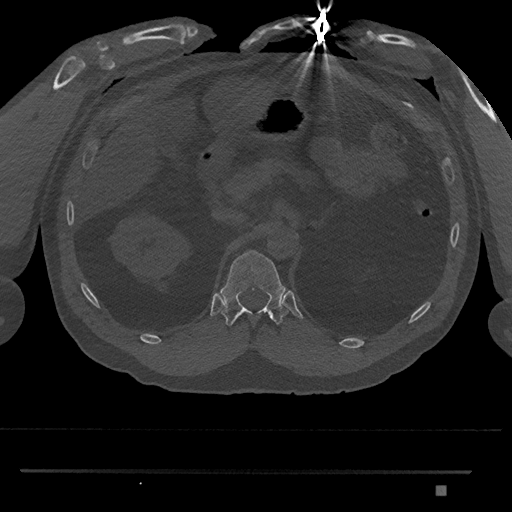
CT including the spine, one axial slice. Slice 895 of 1134 in the series (ordered by position). Reconstruction kernel Br40s/3. 120 kVp. Bone window (W 1800 / L 400 HU). 0.5 mm slice thickness. 512 × 512 image matrix, field of view 429 × 429 mm. Patient: male, 65 years. From the clinical record (not read from this slice): primary cancer: prostate.
Annotated regions visible in this slice (semi-automatically segmented with operator editing):
- T12 vertebra: box from (x=220, y=250) to (x=289, y=327) px